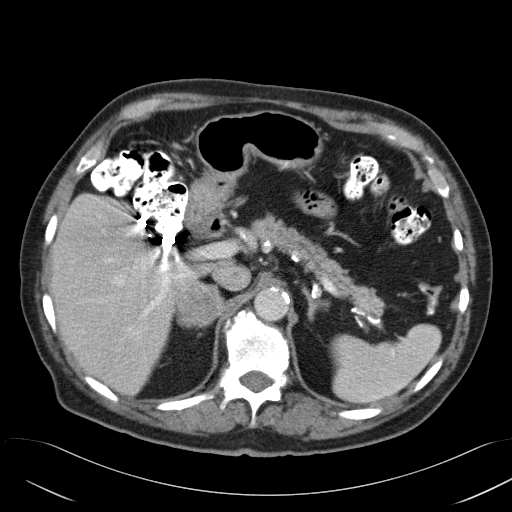
Contrast-enhanced abdominal CT, one axial slice; slice 34 of 58 in the series (ordered by position); reconstruction kernel B31f; 120 kVp; intravenous contrast given; soft-tissue window (W 400 / L 40 HU); 5 mm slice thickness; 512 × 512 image matrix, field of view 384 × 384 mm. Male patient, age 82 years. From the clinical record (not read from this slice): diagnosis: adrenocortical carcinoma; tumour side: right adrenal; tumour size at pathology: 9 cm.
Outlined on this slice (semi-automatic segmentation, software-assisted and operator-edited):
- mass: box from (x=176, y=281) to (x=223, y=331) px